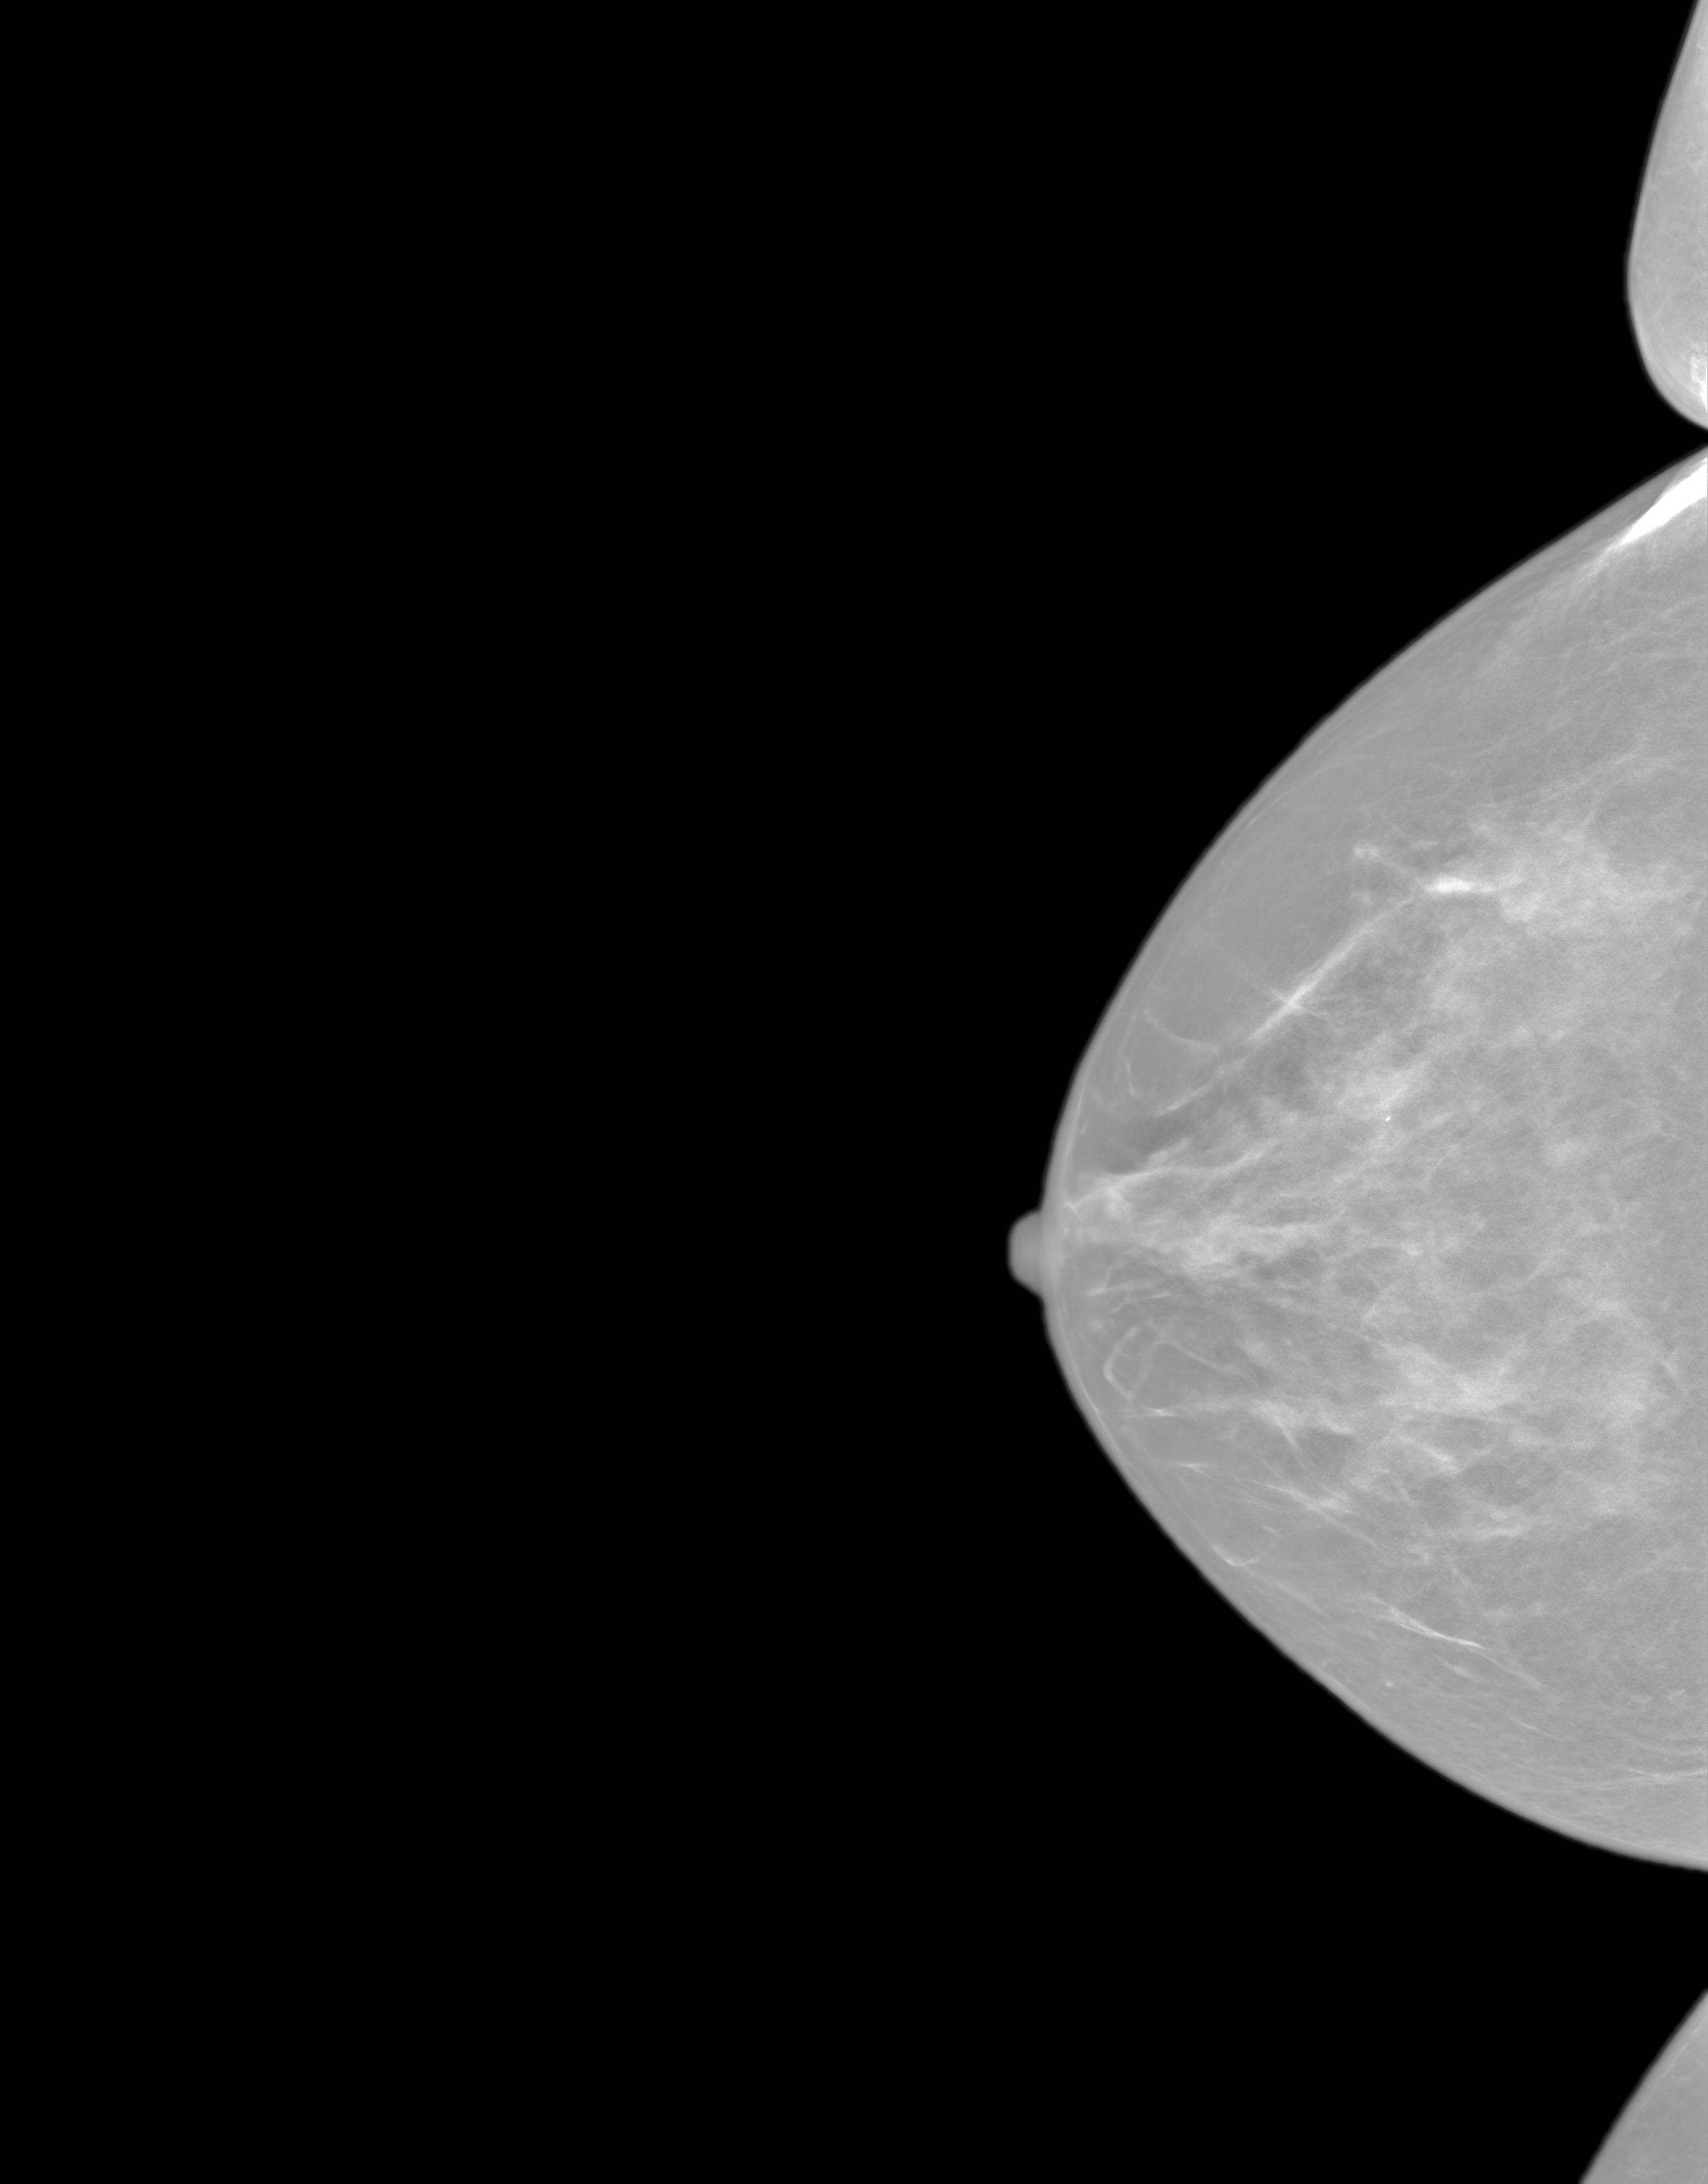
Annual screening mammography examination, system: SenoIris_1SP2(440). Patient aged 46 years (female).
Image type: synthesized 2-D view from tomosynthesis. Breast: right. Projection: cranio-caudal projection.